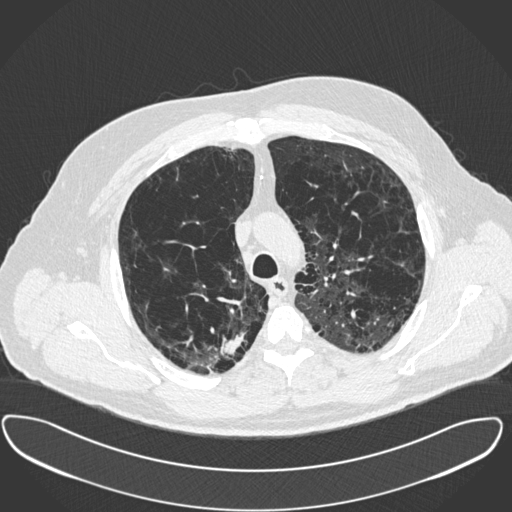
Low-dose screening chest CT, one axial slice. Slice 293 of 385 in the series (ordered by position). Reconstruction kernel B30f. 120 kVp. Lung window (W 1500 / L -600 HU). 1 mm slice thickness. 512 × 512 image matrix, field of view 408 × 408 mm.
Annotated regions visible in this slice (outlined manually by an expert reader):
- lesion 1 (tumor, upper lobe of right lung): bounding box (x1, y1, x2, y2) in pixels: (224, 333, 244, 355)